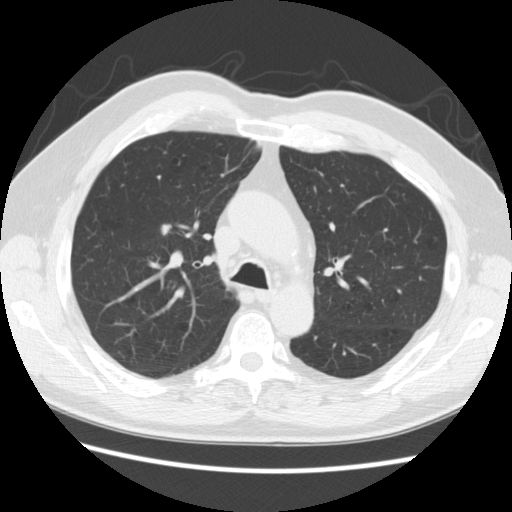
Low-dose screening chest CT, one axial slice. Position 175 of 259 along the scan axis. Lung window (W 1500 / L -600 HU). 2.5 mm slice thickness. 512 × 512 image matrix.
Structures marked on this image (manually delineated by an expert):
- lesion 1 (tumor, upper lobe of right lung): bounding box <161,224,172,235> (left, top, right, bottom; pixels)